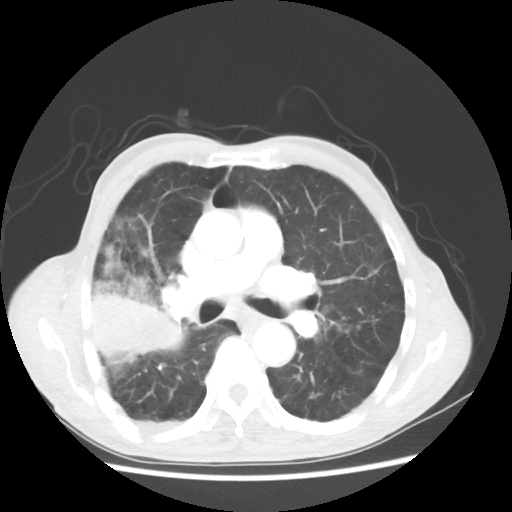
Chest CT, one axial slice; slice 31 of 58 in the series (ordered by position); reconstruction kernel STANDARD; 100 kVp; lung window (W 1500 / L -600 HU); 5 mm slice thickness; 512 × 512 image matrix, field of view 351 × 351 mm. Male patient, age 75 years. From the clinical record (not read from this slice): clinical TNM (as recorded): T4 N1 M1.
Annotated regions visible in this slice (rectangle marked by the reading radiologist):
- lung tumour (recorded histology: adenocarcinoma): bounding box (x1, y1, x2, y2) in pixels: (78, 264, 190, 361)